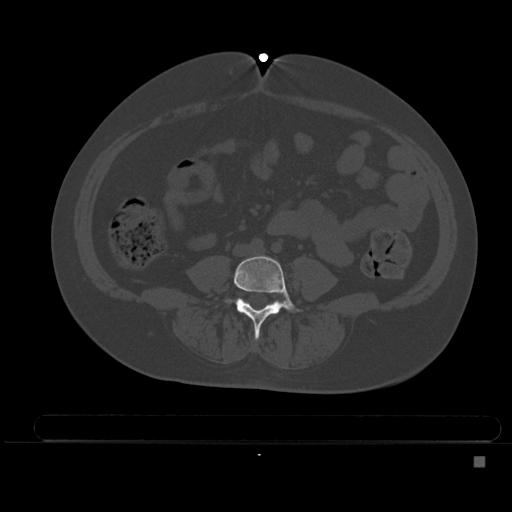
CT including the spine, one axial slice; position 128 of 495 along the scan axis; bone window (W 1800 / L 400 HU); 1.5 mm slice thickness; 512 × 512 image matrix. Female patient, age 33 years. From the clinical record (not read from this slice): primary cancer: breast.
Annotated regions visible in this slice (semi-automatically segmented with operator editing):
- L4 vertebra: bounding box (x1, y1, x2, y2) in pixels: (224, 255, 303, 339)